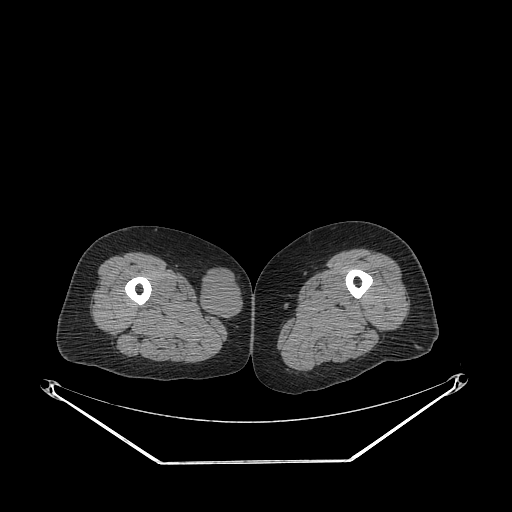
CT of an extremity soft-tissue mass (from a PET/CT study), one axial slice; slice 232 of 311 in the series (ordered by position); 140 kVp; soft-tissue window (W 400 / L 40 HU); 512 × 512 image matrix. Female patient. From the clinical record (not read from this slice): histological type: leiomyosarcoma; grade: intermediate; site of the primary tumour: parascapusular.
Structures marked on this image (expert contour drawn on MRI and transferred to this co-registered scan by the dataset authors):
- gross tumour volume including surrounding oedema: bounding box [x1, y1, x2, y2] px = [201, 267, 241, 323]
- gross tumour volume (mass): [201, 267, 241, 321]